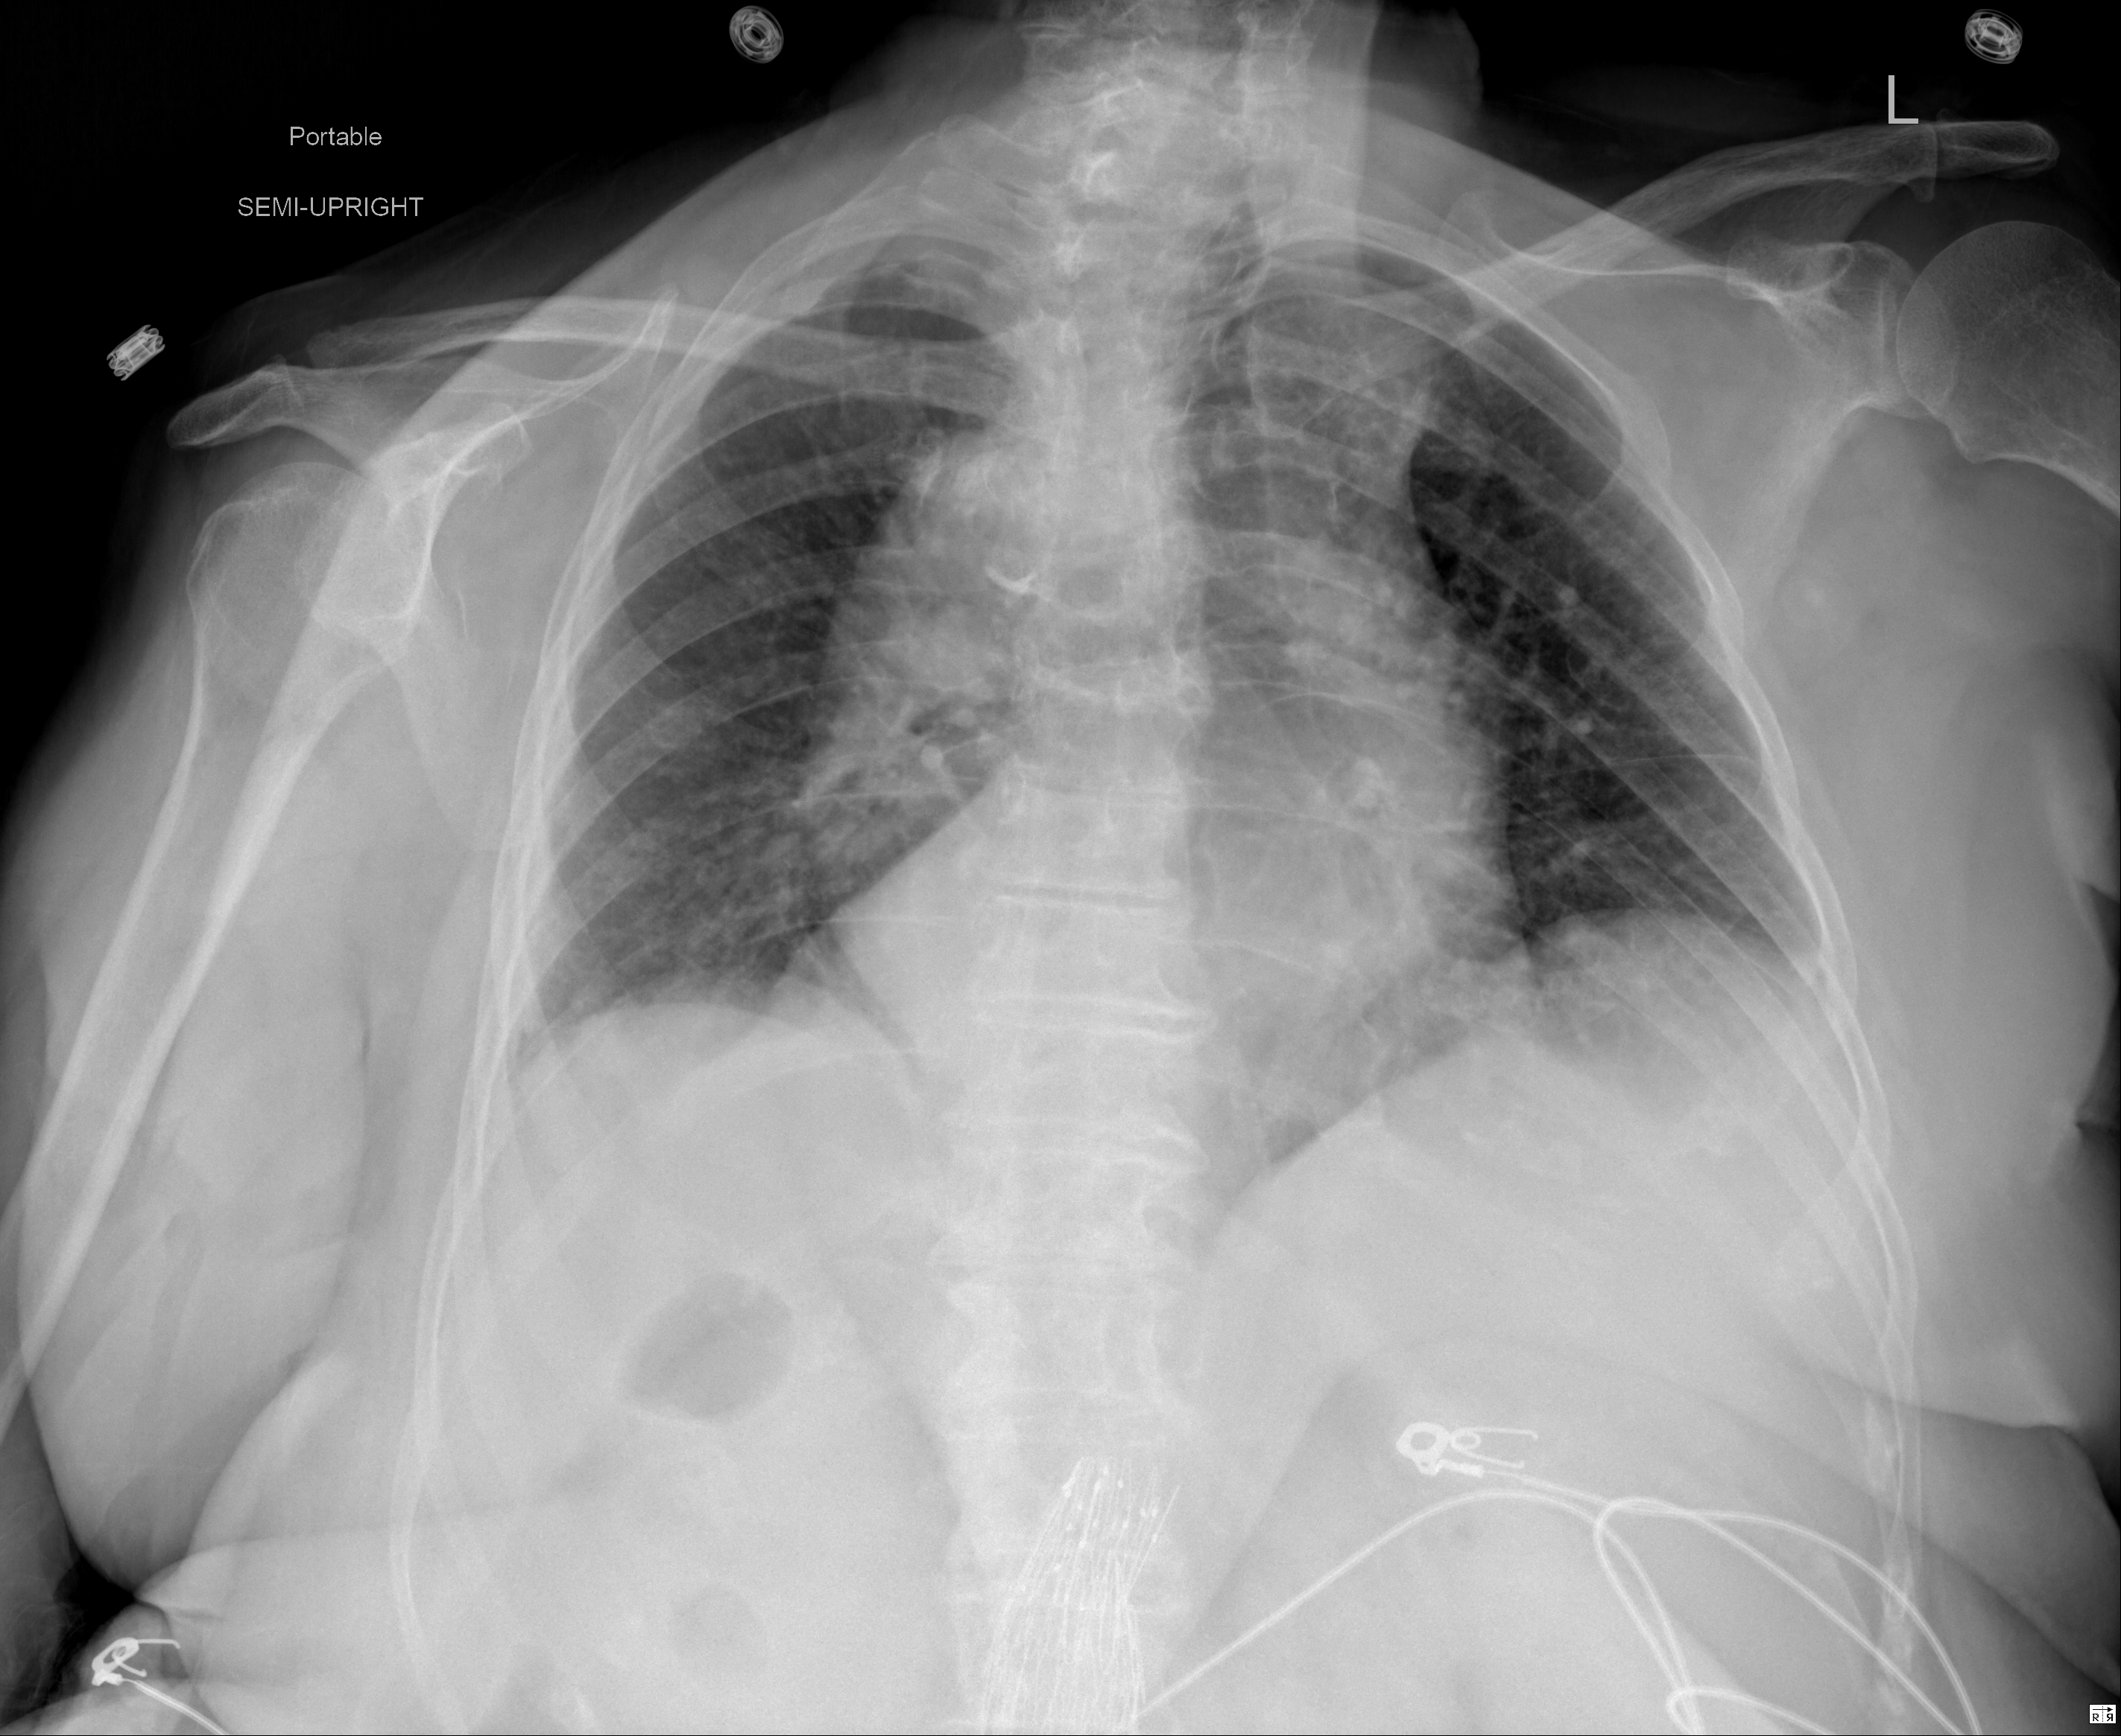
Chest X-ray, PA projection. Female patient, age 88 years; imaged 2 days after the COVID-19 diagnosis.
Key findings recorded by the radiologist: Low lung volumes with minimal bibasilar subsegmental atelectasis.